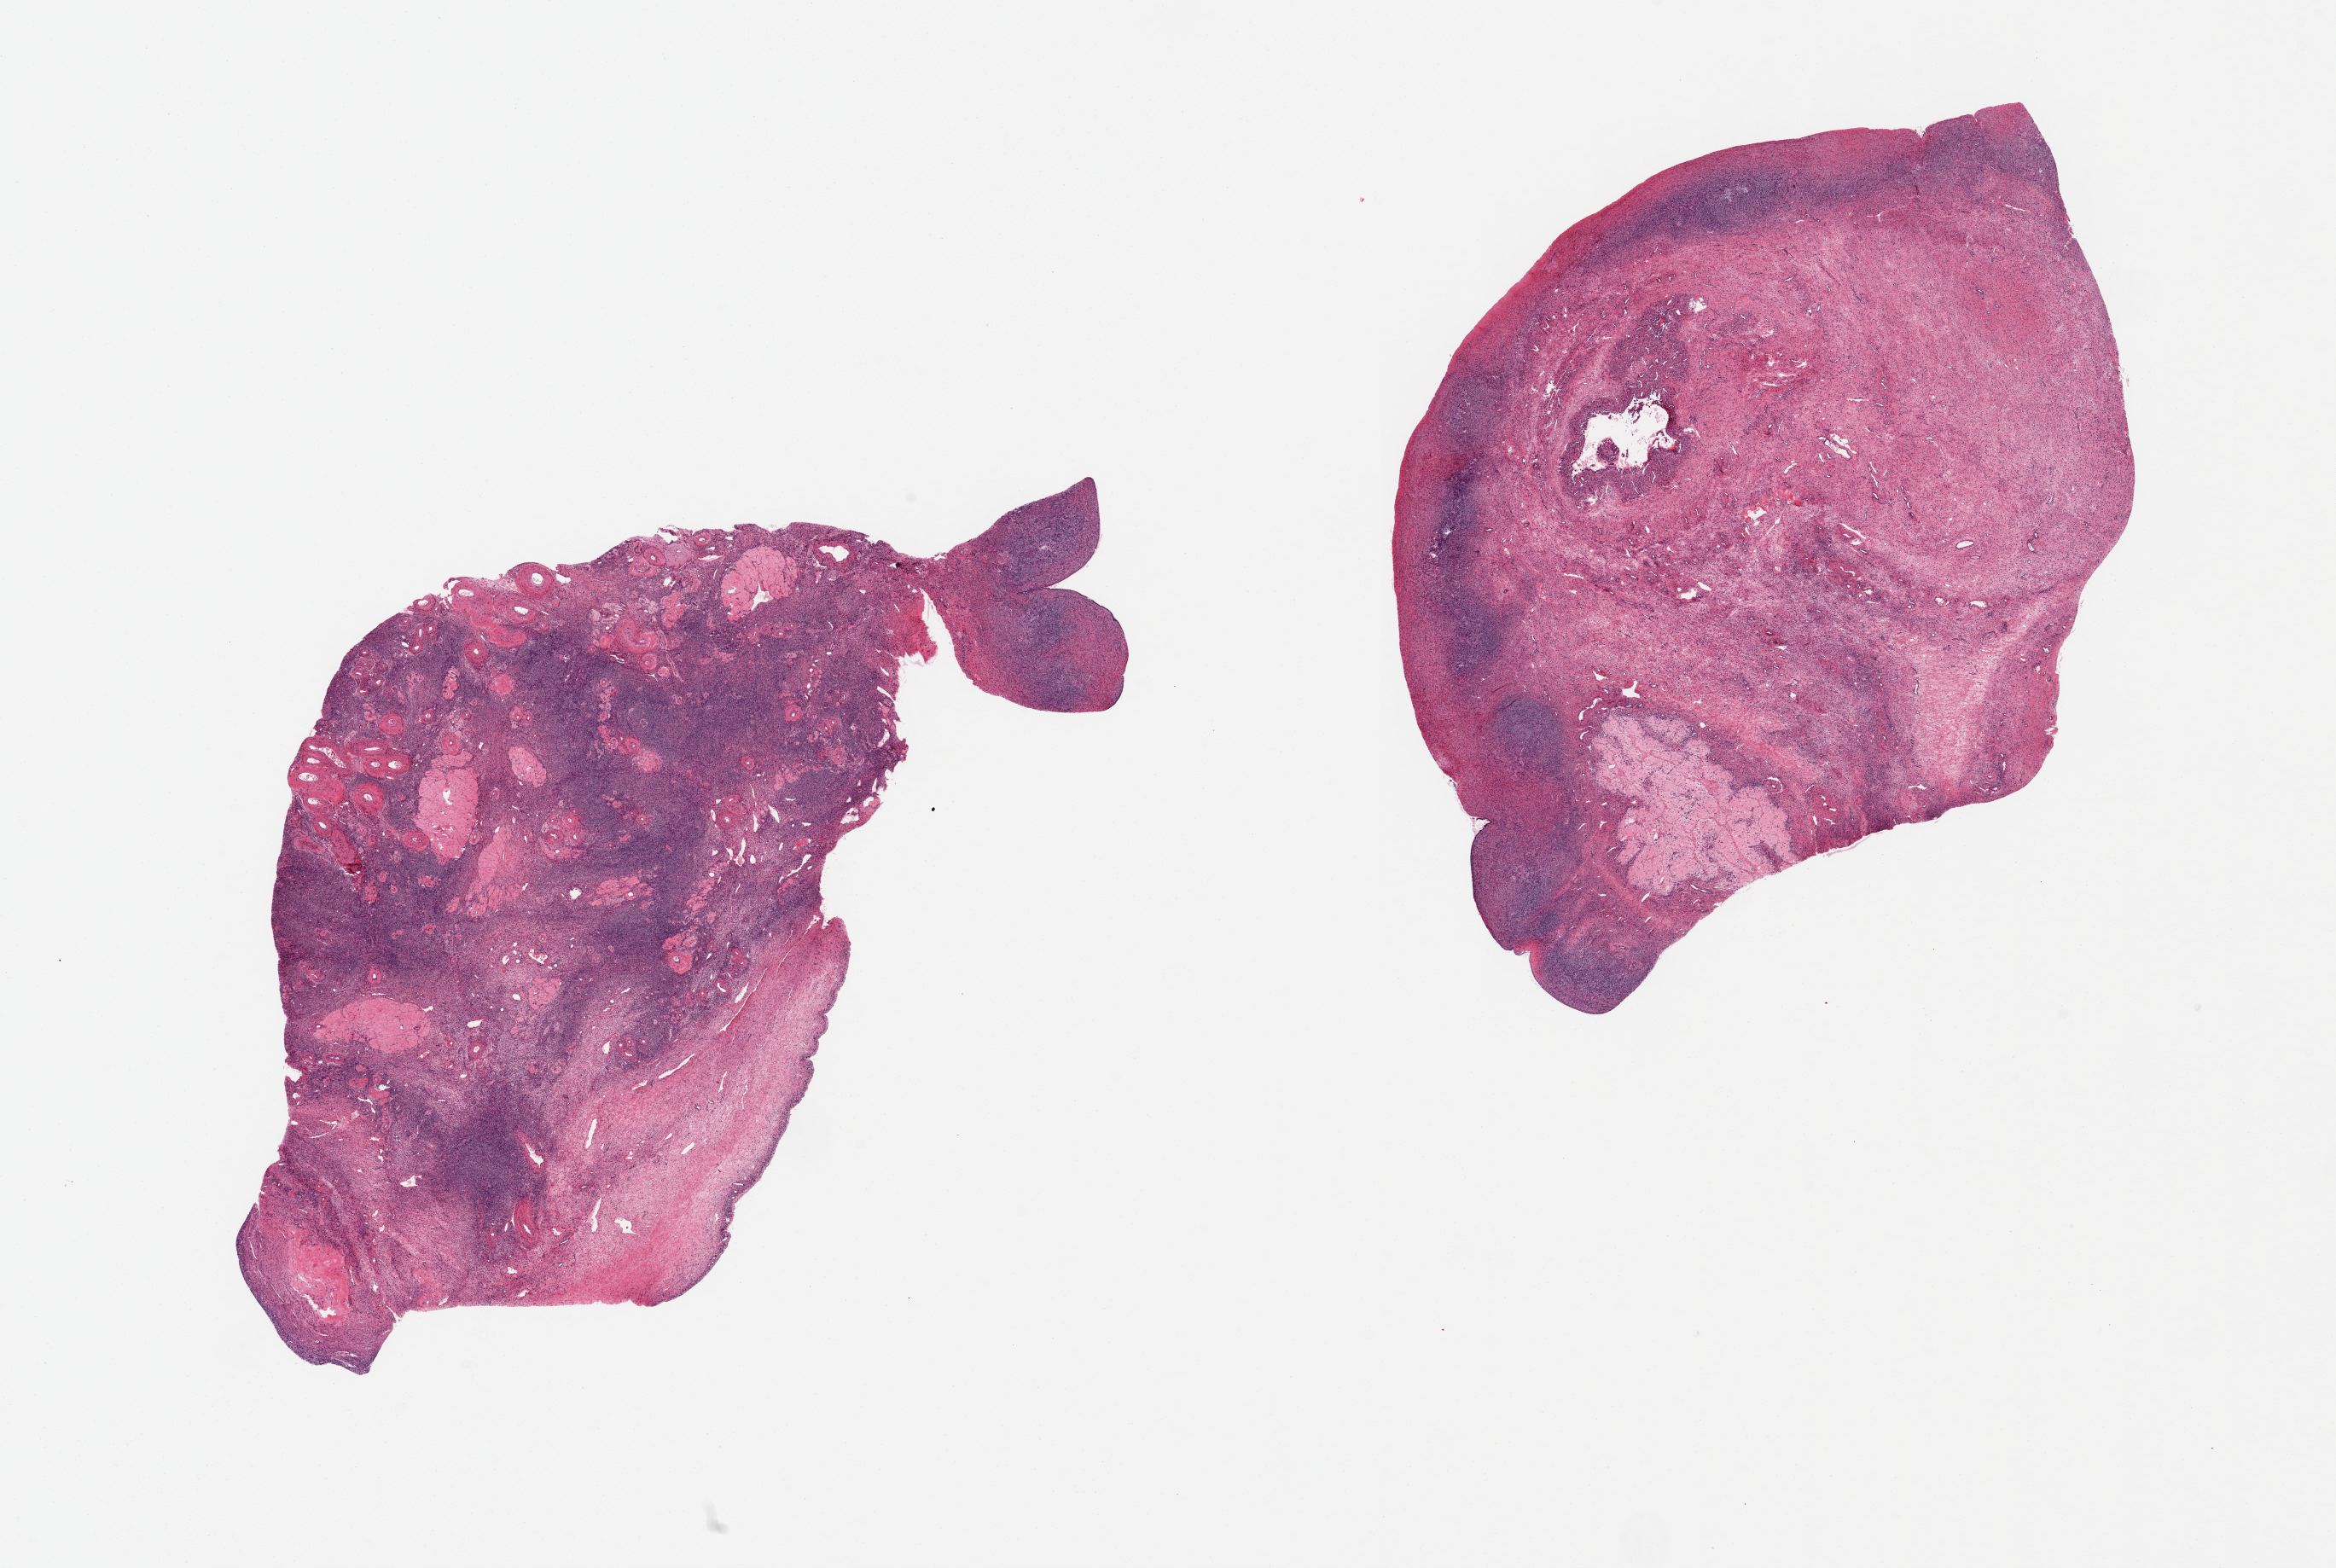
Digitized haematoxylin and eosin-stained section, whole scanned area (about 21.7 x 14.5 mm, acquisition: 20x scan) shown as a low-resolution overview; PAXgene-fixed paraffin-embedded (PFPE) section; sampled site (target tissue): ovary; tissue donor sample. Female donor.
Reviewer comment on this tissue sample: 2 pieces 9x6 & 9x6 mm; corppora albicantia.